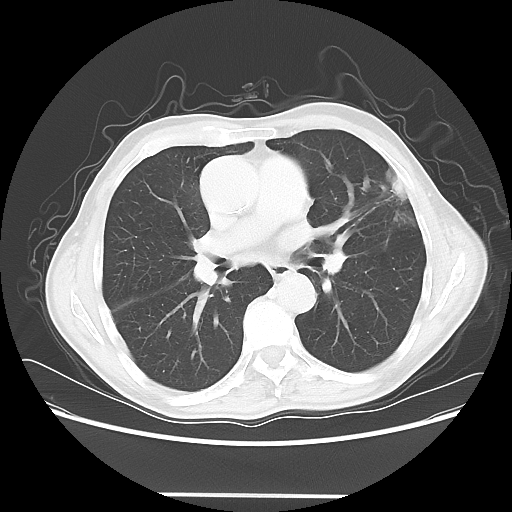
Chest CT, one axial slice. Position 35 of 64 along the scan axis. Reconstruction kernel LUNG. 120 kVp. Lung window (W 1500 / L -600 HU). 512 × 512 image matrix, field of view 392 × 392 mm. Patient: male, 71 years. Case-level facts recorded for this patient, not image findings: clinical TNM (as recorded): T1c N0 M0; histopathological grade: G2-3.
Outlined on this slice (rectangle marked by the reading radiologist):
- lung tumour (recorded histology: adenocarcinoma): box from (x=385, y=166) to (x=409, y=198) px